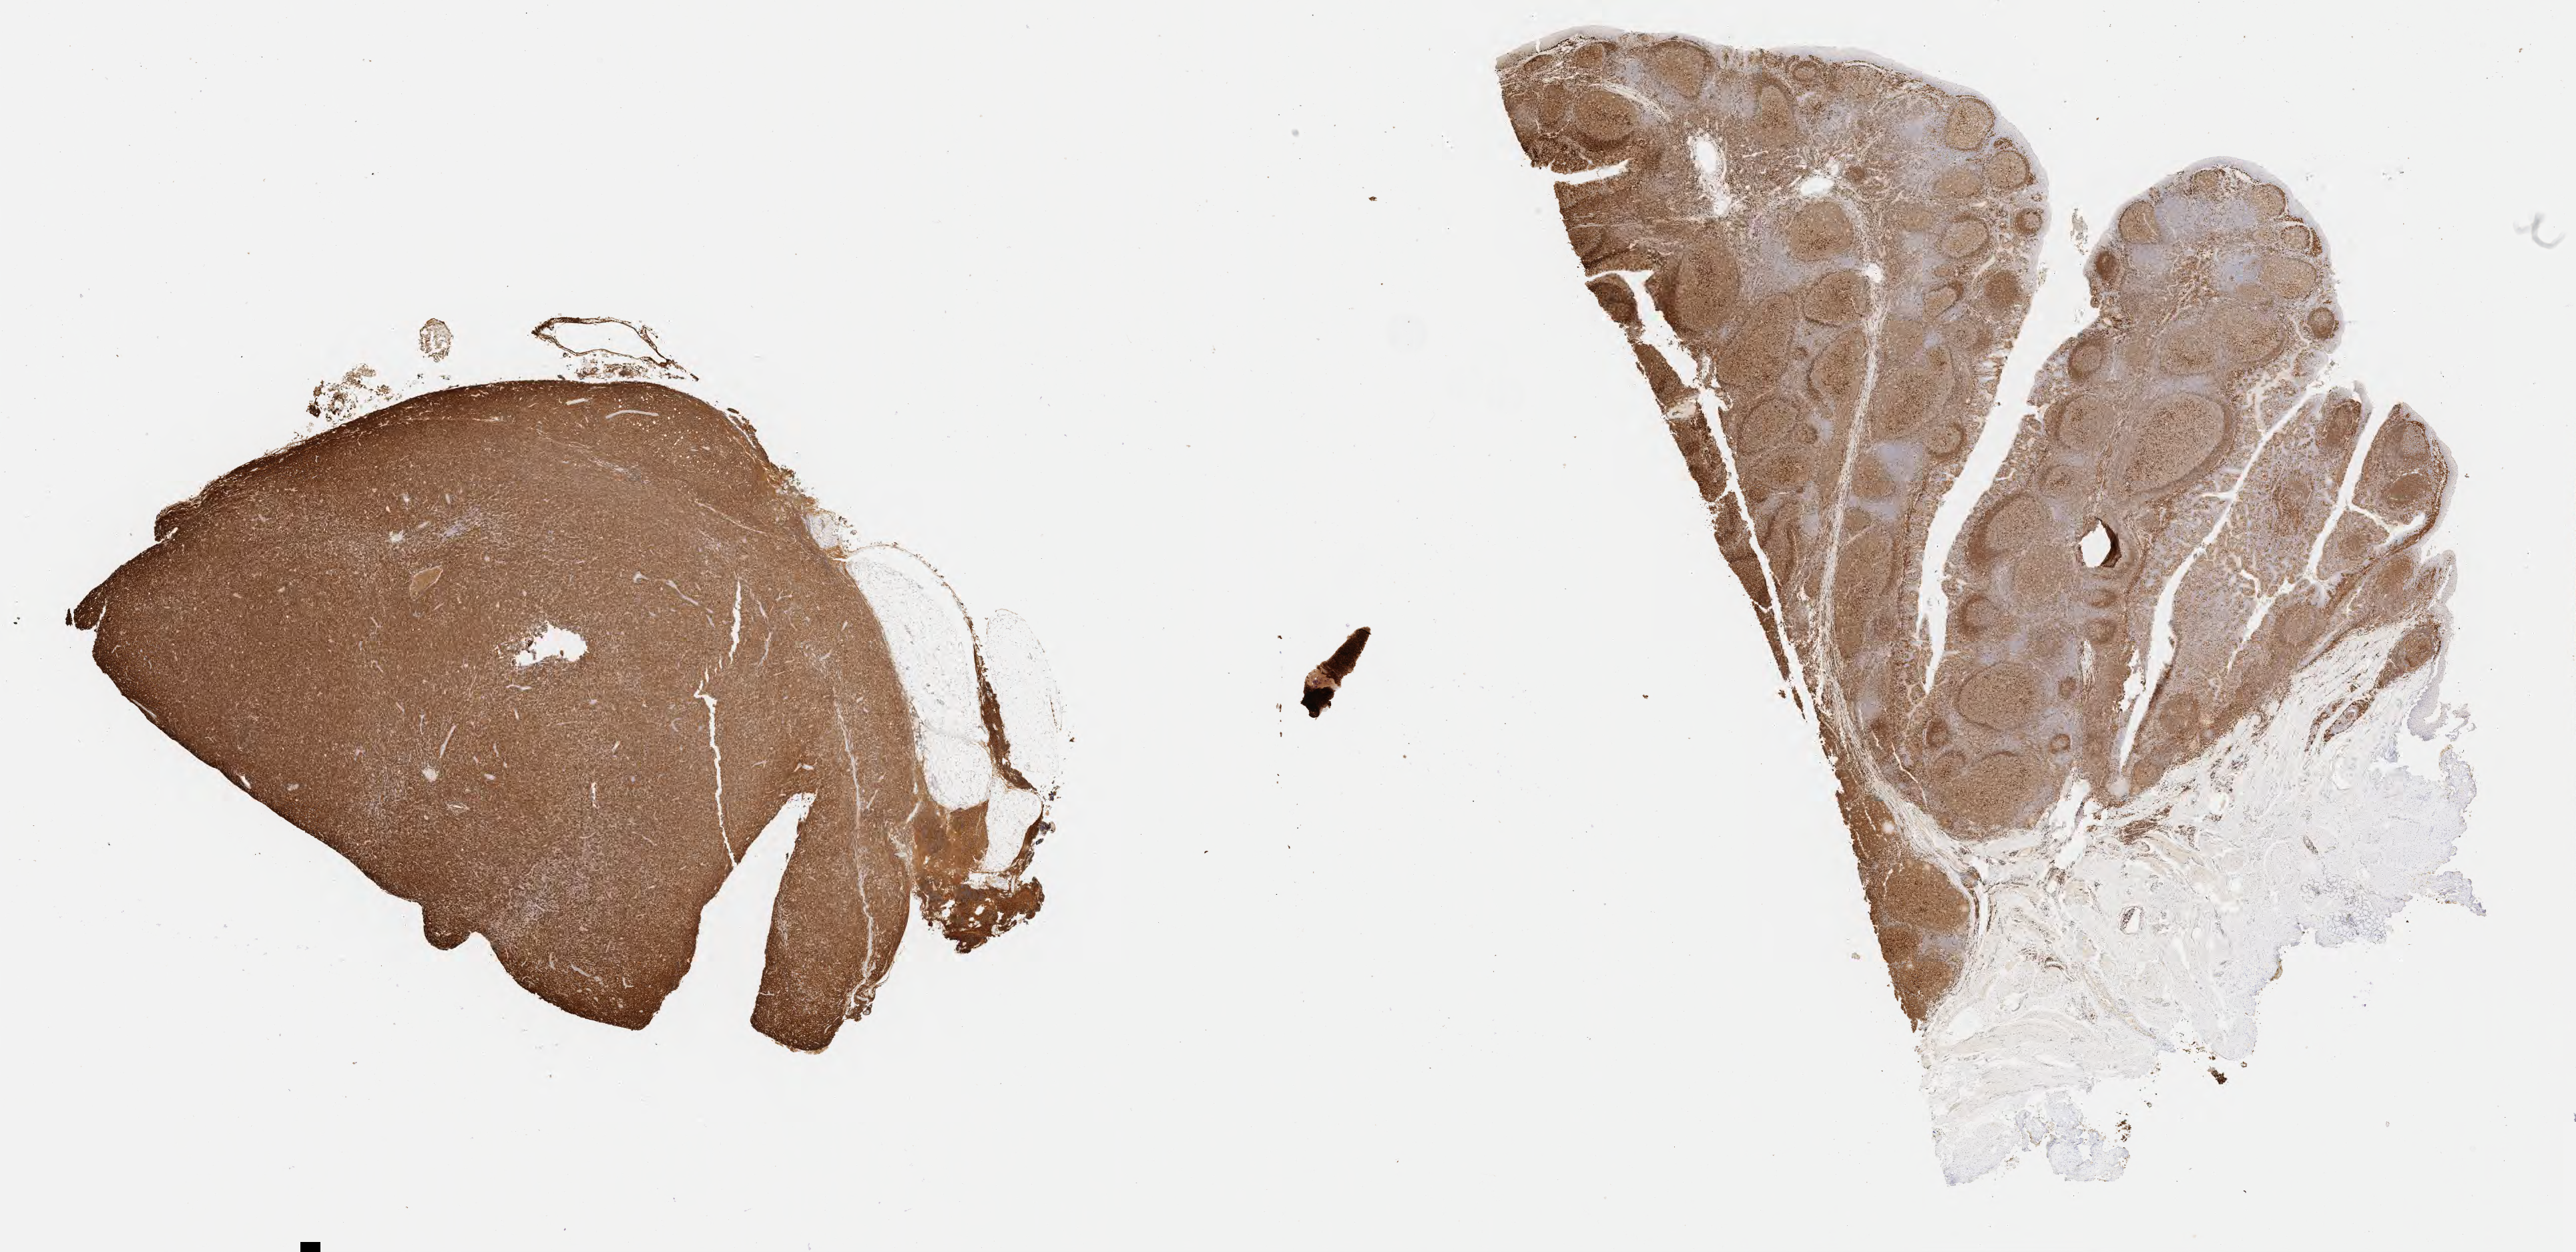
Immunohistochemistry (IHC) whole-slide image stained for CD79a, shown as a low-resolution overview of the whole scanned area (about 31.2 x 15.2 mm), specimen: tumor tissue, site: lymph node. Patient male; 26 years old.
Histologic diagnosis: Diffuse large B-cell lymphoma, NOS.